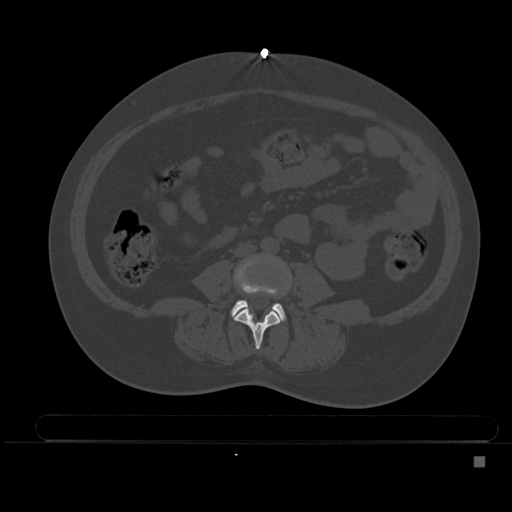
CT including the spine, one axial slice. Position 140 of 495 along the scan axis. Bone window (W 1800 / L 400 HU). 512 × 512 image matrix, field of view 404 × 404 mm. Female patient, age 33 years. Case-level facts recorded for this patient, not image findings: primary cancer: breast.
Outlined on this slice (semi-automatically segmented with operator editing):
- L3 vertebra: box from (x=234, y=307) to (x=282, y=350) px
- L4 vertebra: (x=231, y=260)–(x=286, y=320)